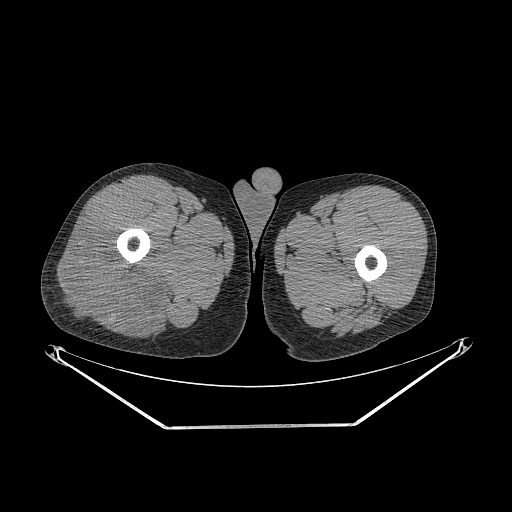
CT of an extremity soft-tissue mass (from a PET/CT study), one axial slice. Reconstruction kernel STANDARD. 140 kVp. Soft-tissue window (W 400 / L 40 HU). 3.75 mm slice thickness. 512 × 512 image matrix, field of view 500 × 500 mm. Male patient. From the clinical record (not read from this slice): histological type: poorly differentiated synovial sarcoma; grade: high; site of the primary tumour: right buttock.
Structures marked on this image (expert contour drawn on MRI and transferred to this co-registered scan by the dataset authors):
- gross tumour volume including surrounding oedema: bounding box [x1, y1, x2, y2] px = [55, 219, 175, 334]
- gross tumour volume (mass): [55, 219, 161, 334]